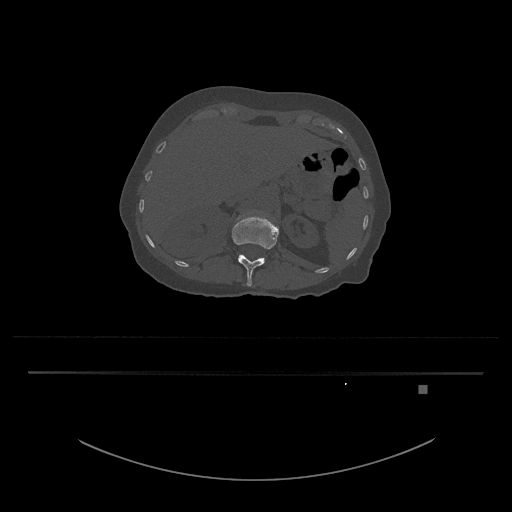
CT including the spine, one axial slice. Slice 543 of 797 in the series (ordered by position). 120 kVp. Bone window (W 1800 / L 400 HU). 0.5 mm slice thickness. 512 × 512 image matrix. Female patient, age 57 years. From the clinical record (not read from this slice): primary cancer: cervical.
Annotated regions visible in this slice (semi-automatically segmented with operator editing):
- L1 vertebra: bounding box [x1, y1, x2, y2] px = [231, 216, 279, 287]